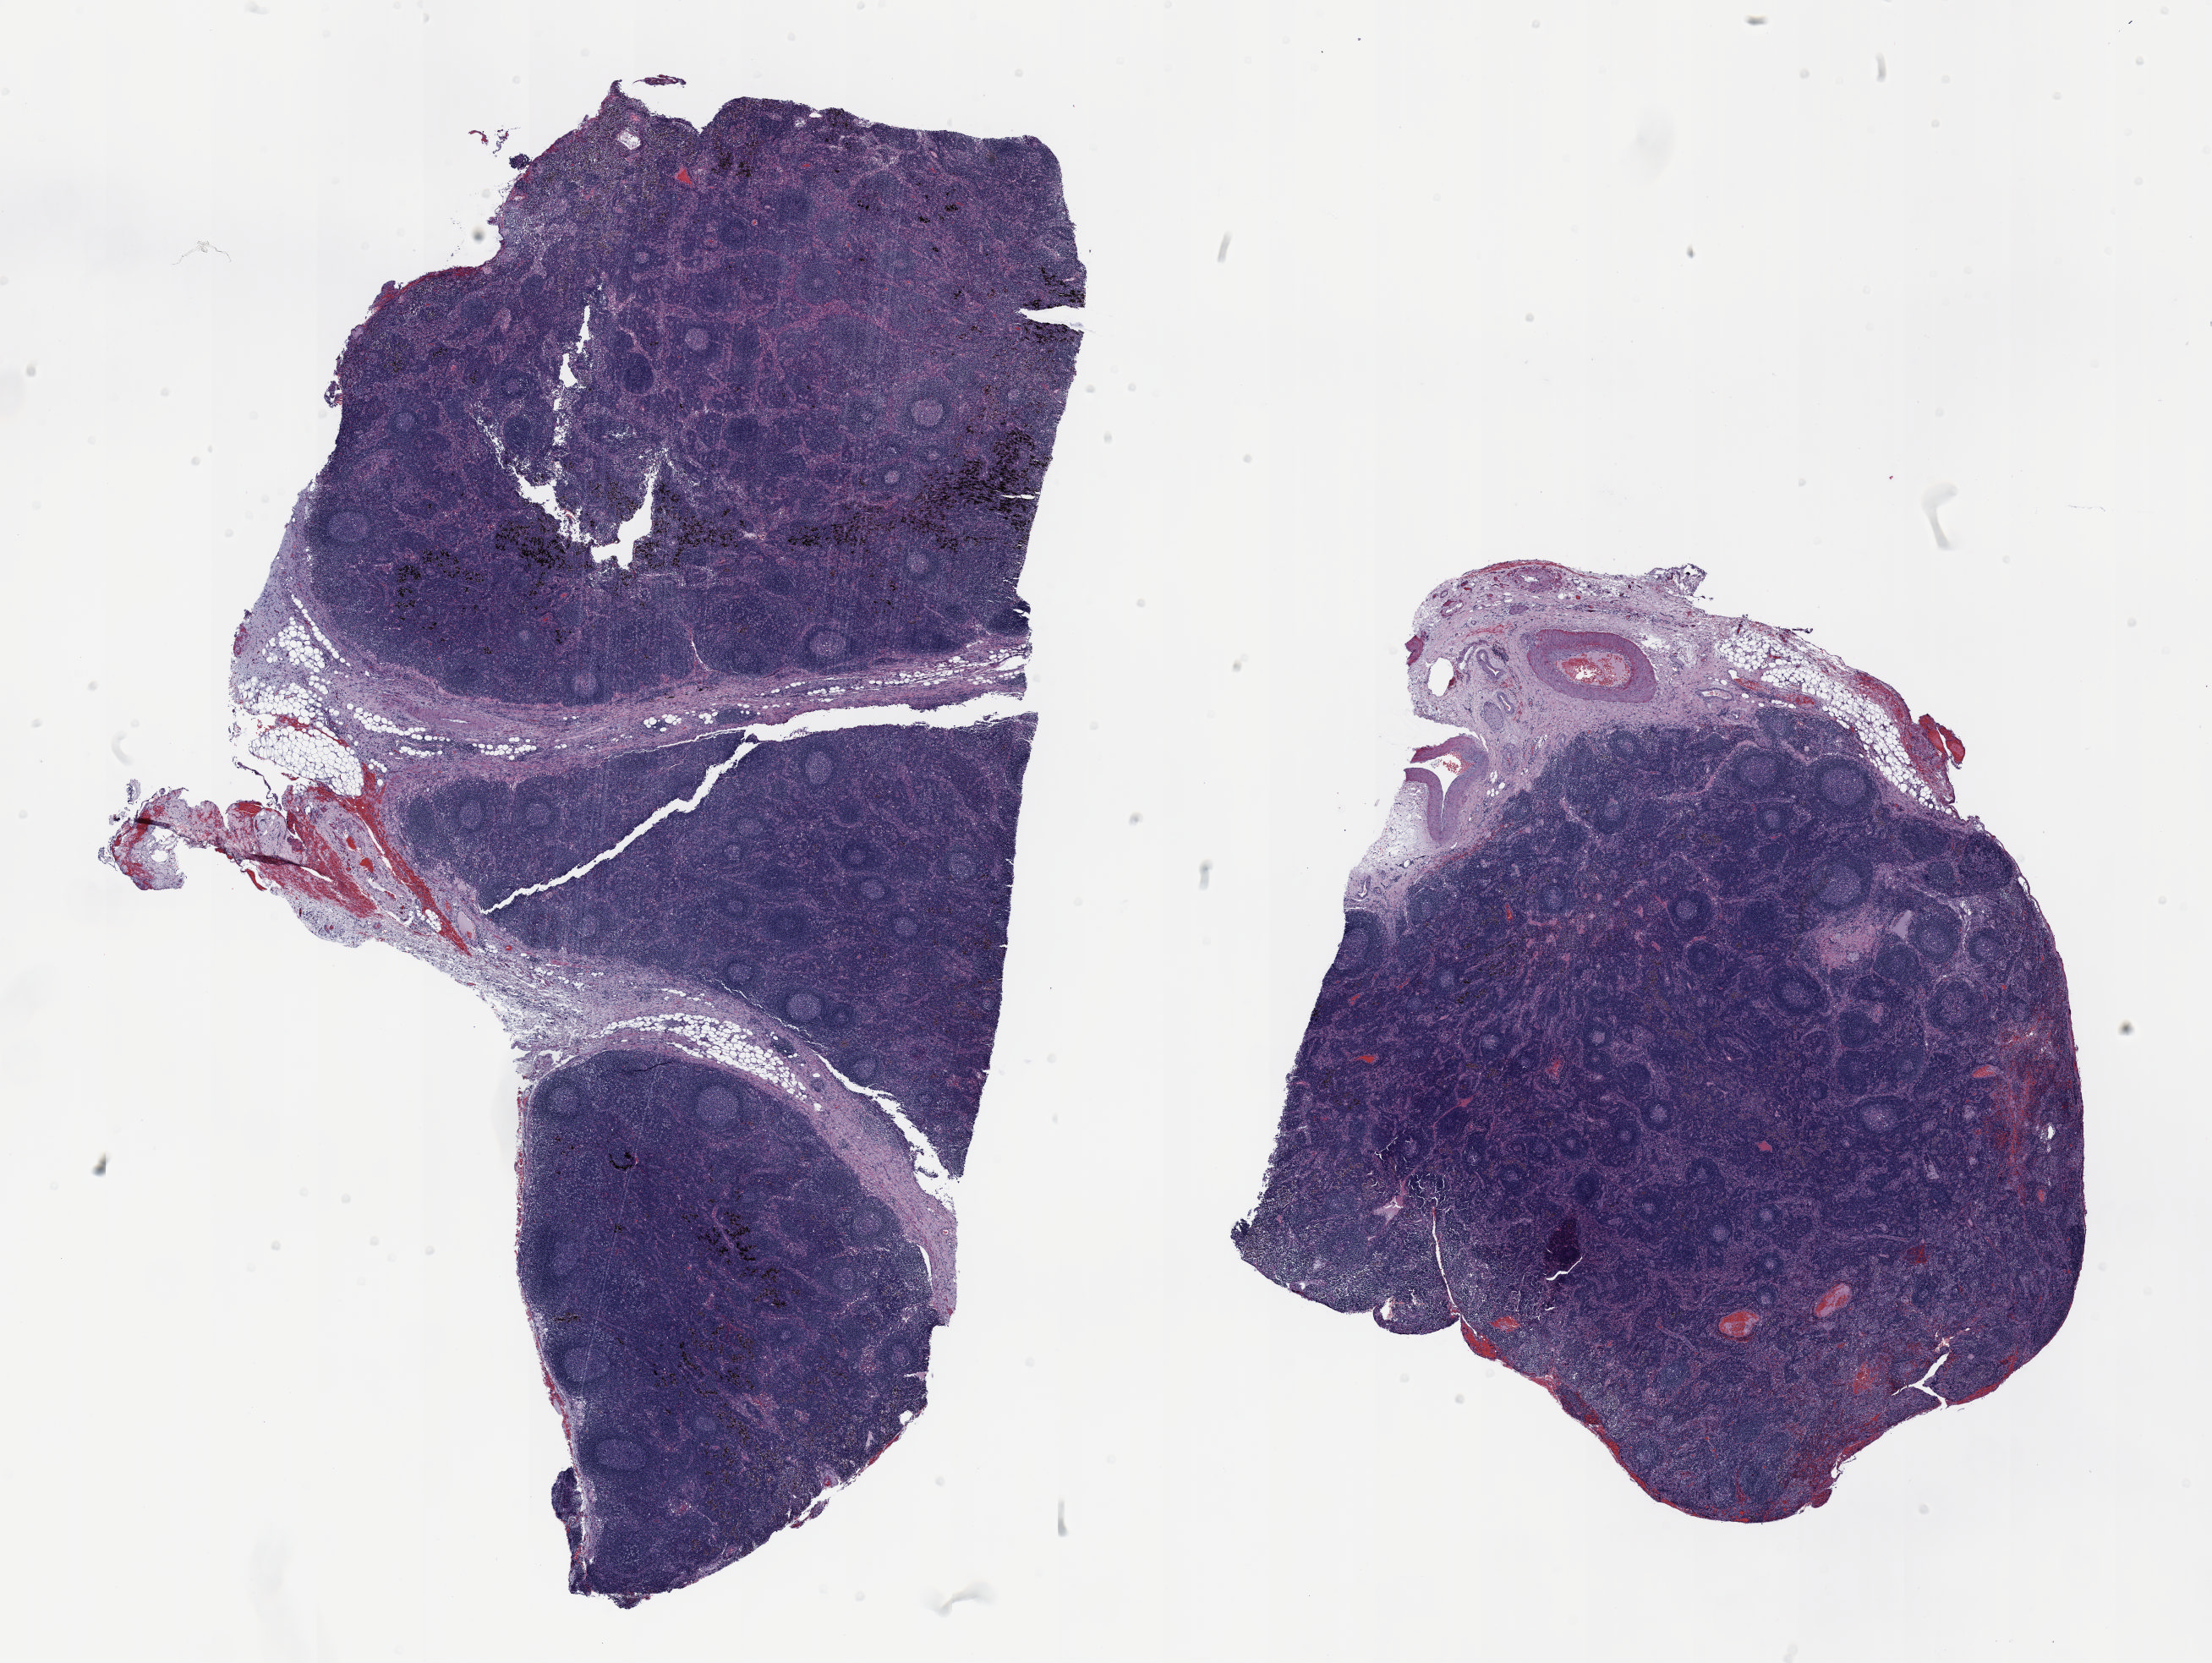
Hematoxylin and eosin (H&E) stained whole-slide image, low-resolution overview of the scanned area, about 21.0 x 15.8 mm (from a 20x scan); formalin-fixed paraffin-embedded (FFPE) section; lung tissue. Male, age 55 at enrolment. Grade: poorly differentiated (G3).
- stage (AJCC 6th edition): IIB
- tumour size (pathology): 115 mm
- participant's lung-cancer diagnosis: Adenocarcinoma, NOS
- primary tumour location (clinical record): right upper lobe